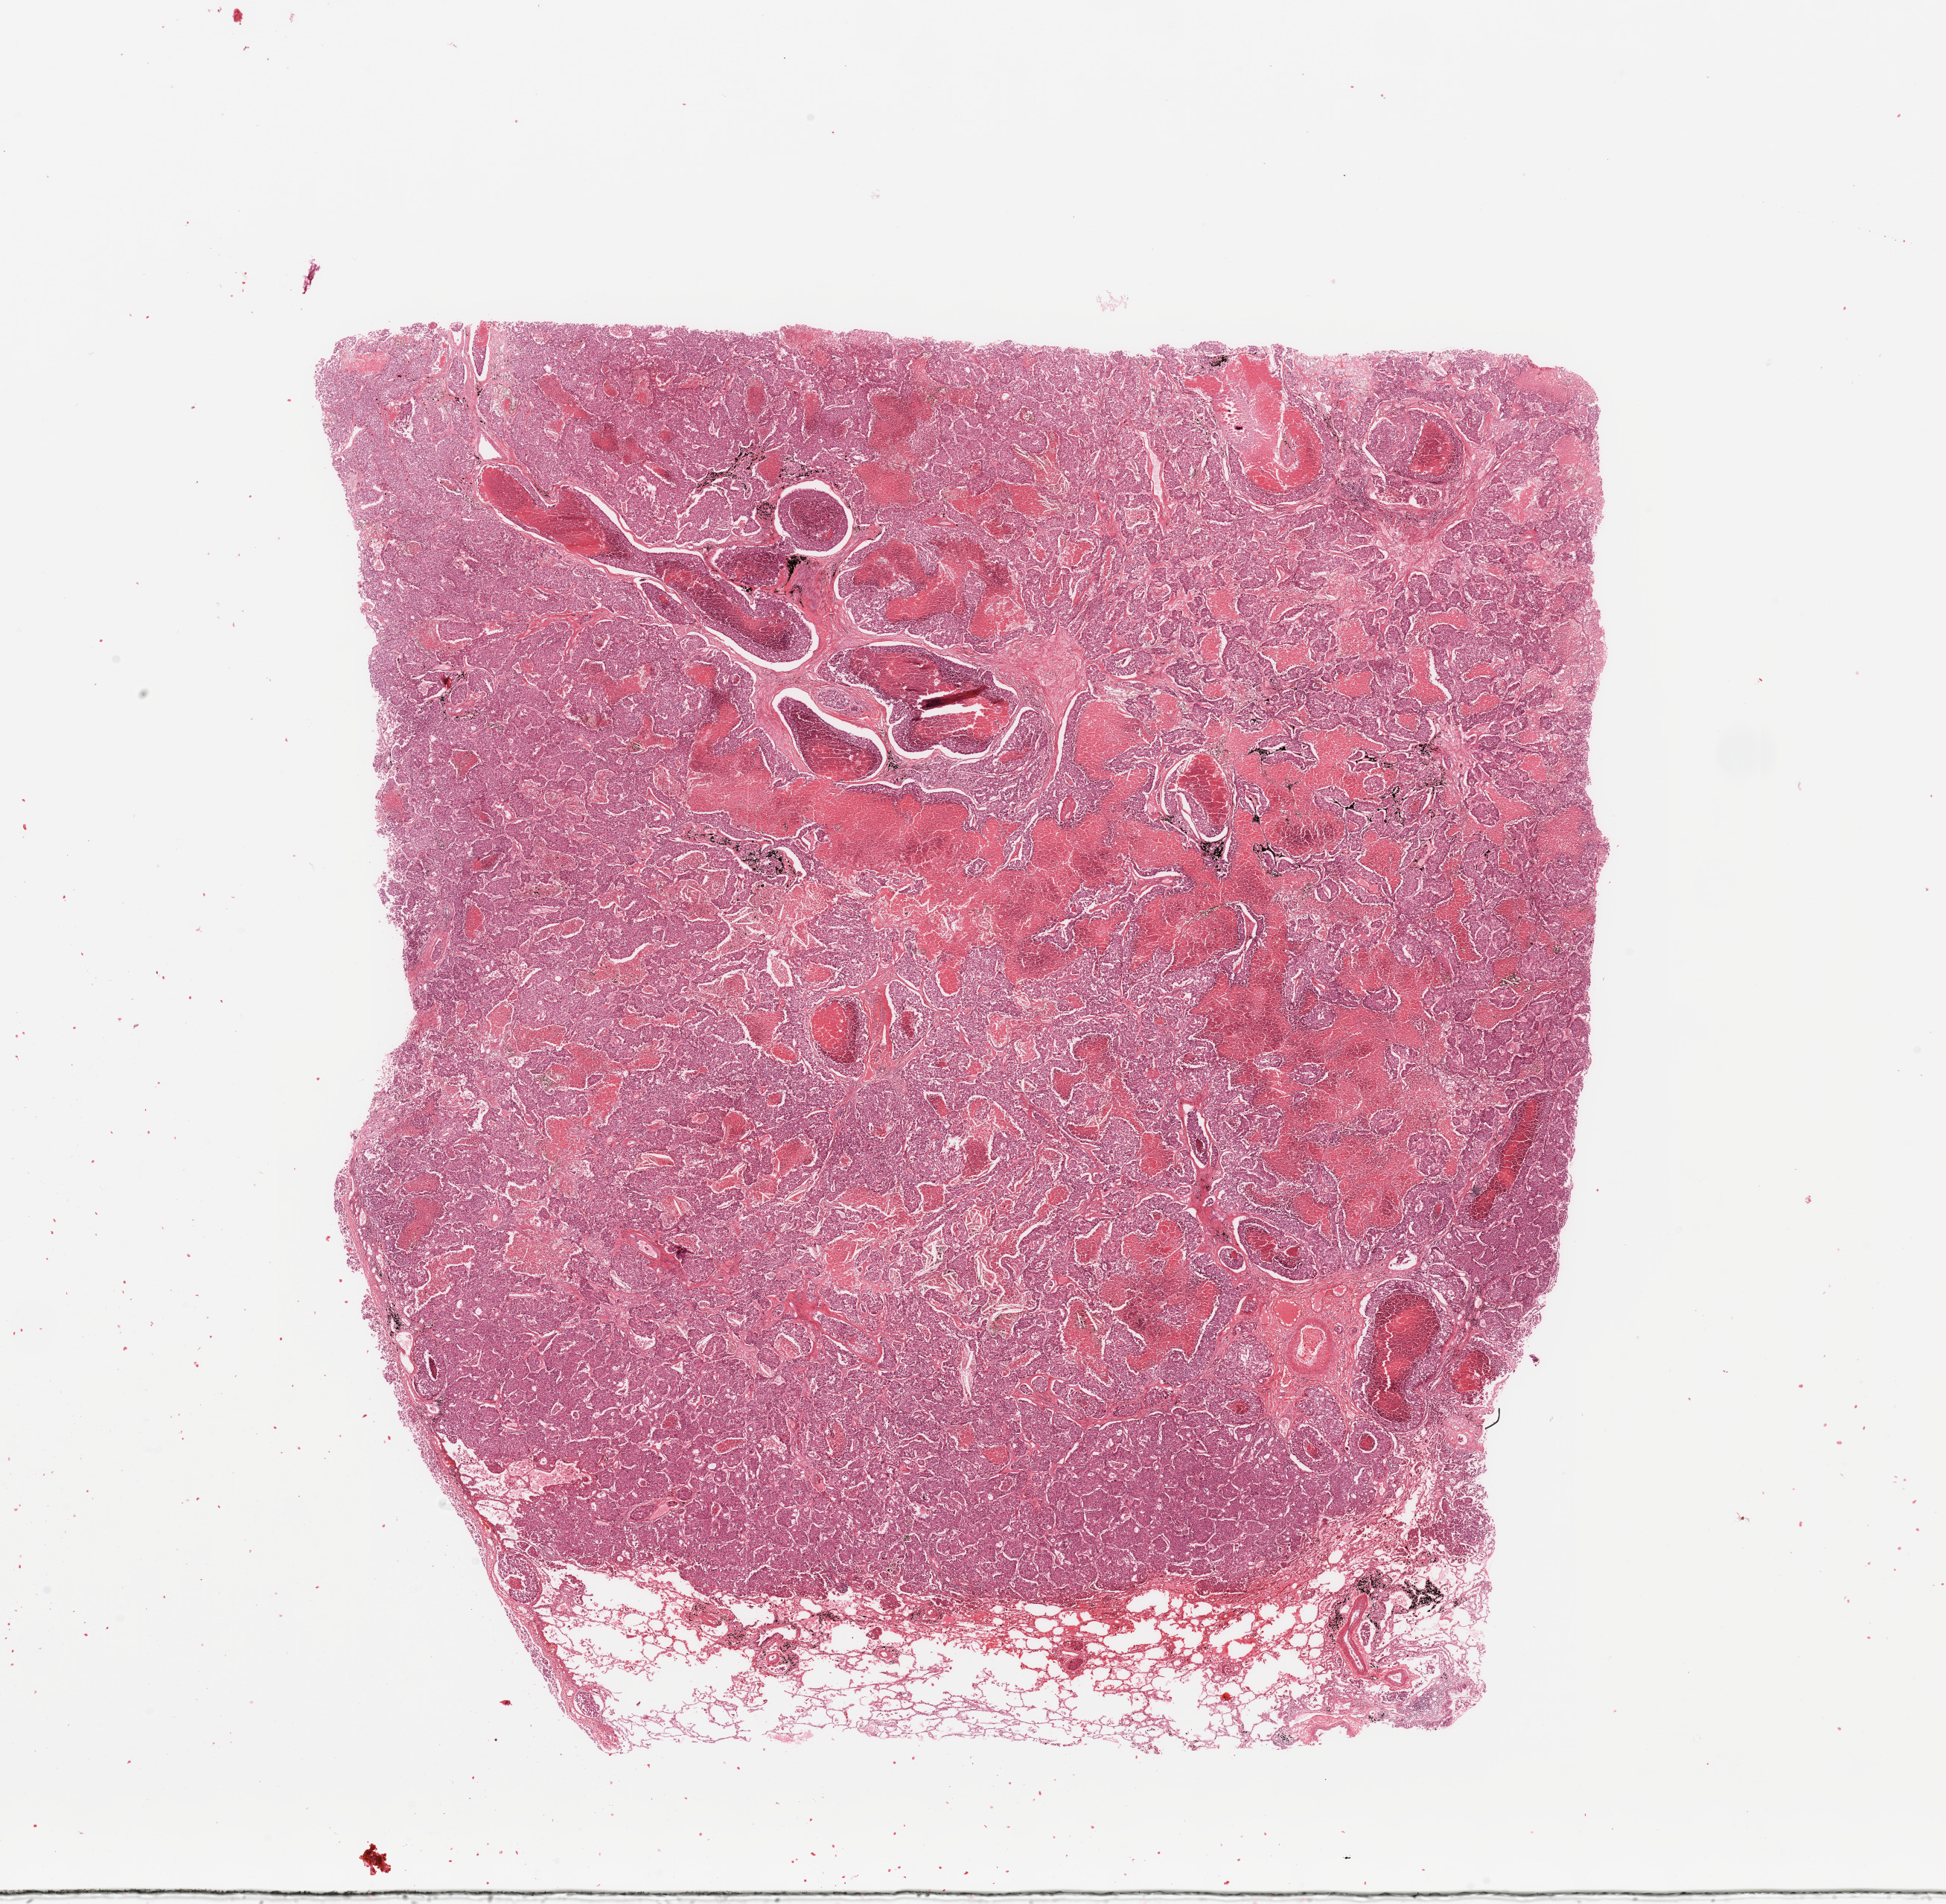
Whole-slide histology image, H&E — shown as a low-resolution overview of the whole scanned area (about 20.7 x 20.2 mm); tumour tissue sample, lung. 56-year-old male patient. Histologic grade: G3 (poorly differentiated).
• diagnosis: Adenocarcinoma, NOS
• AJCC pathologic stage: IIIA